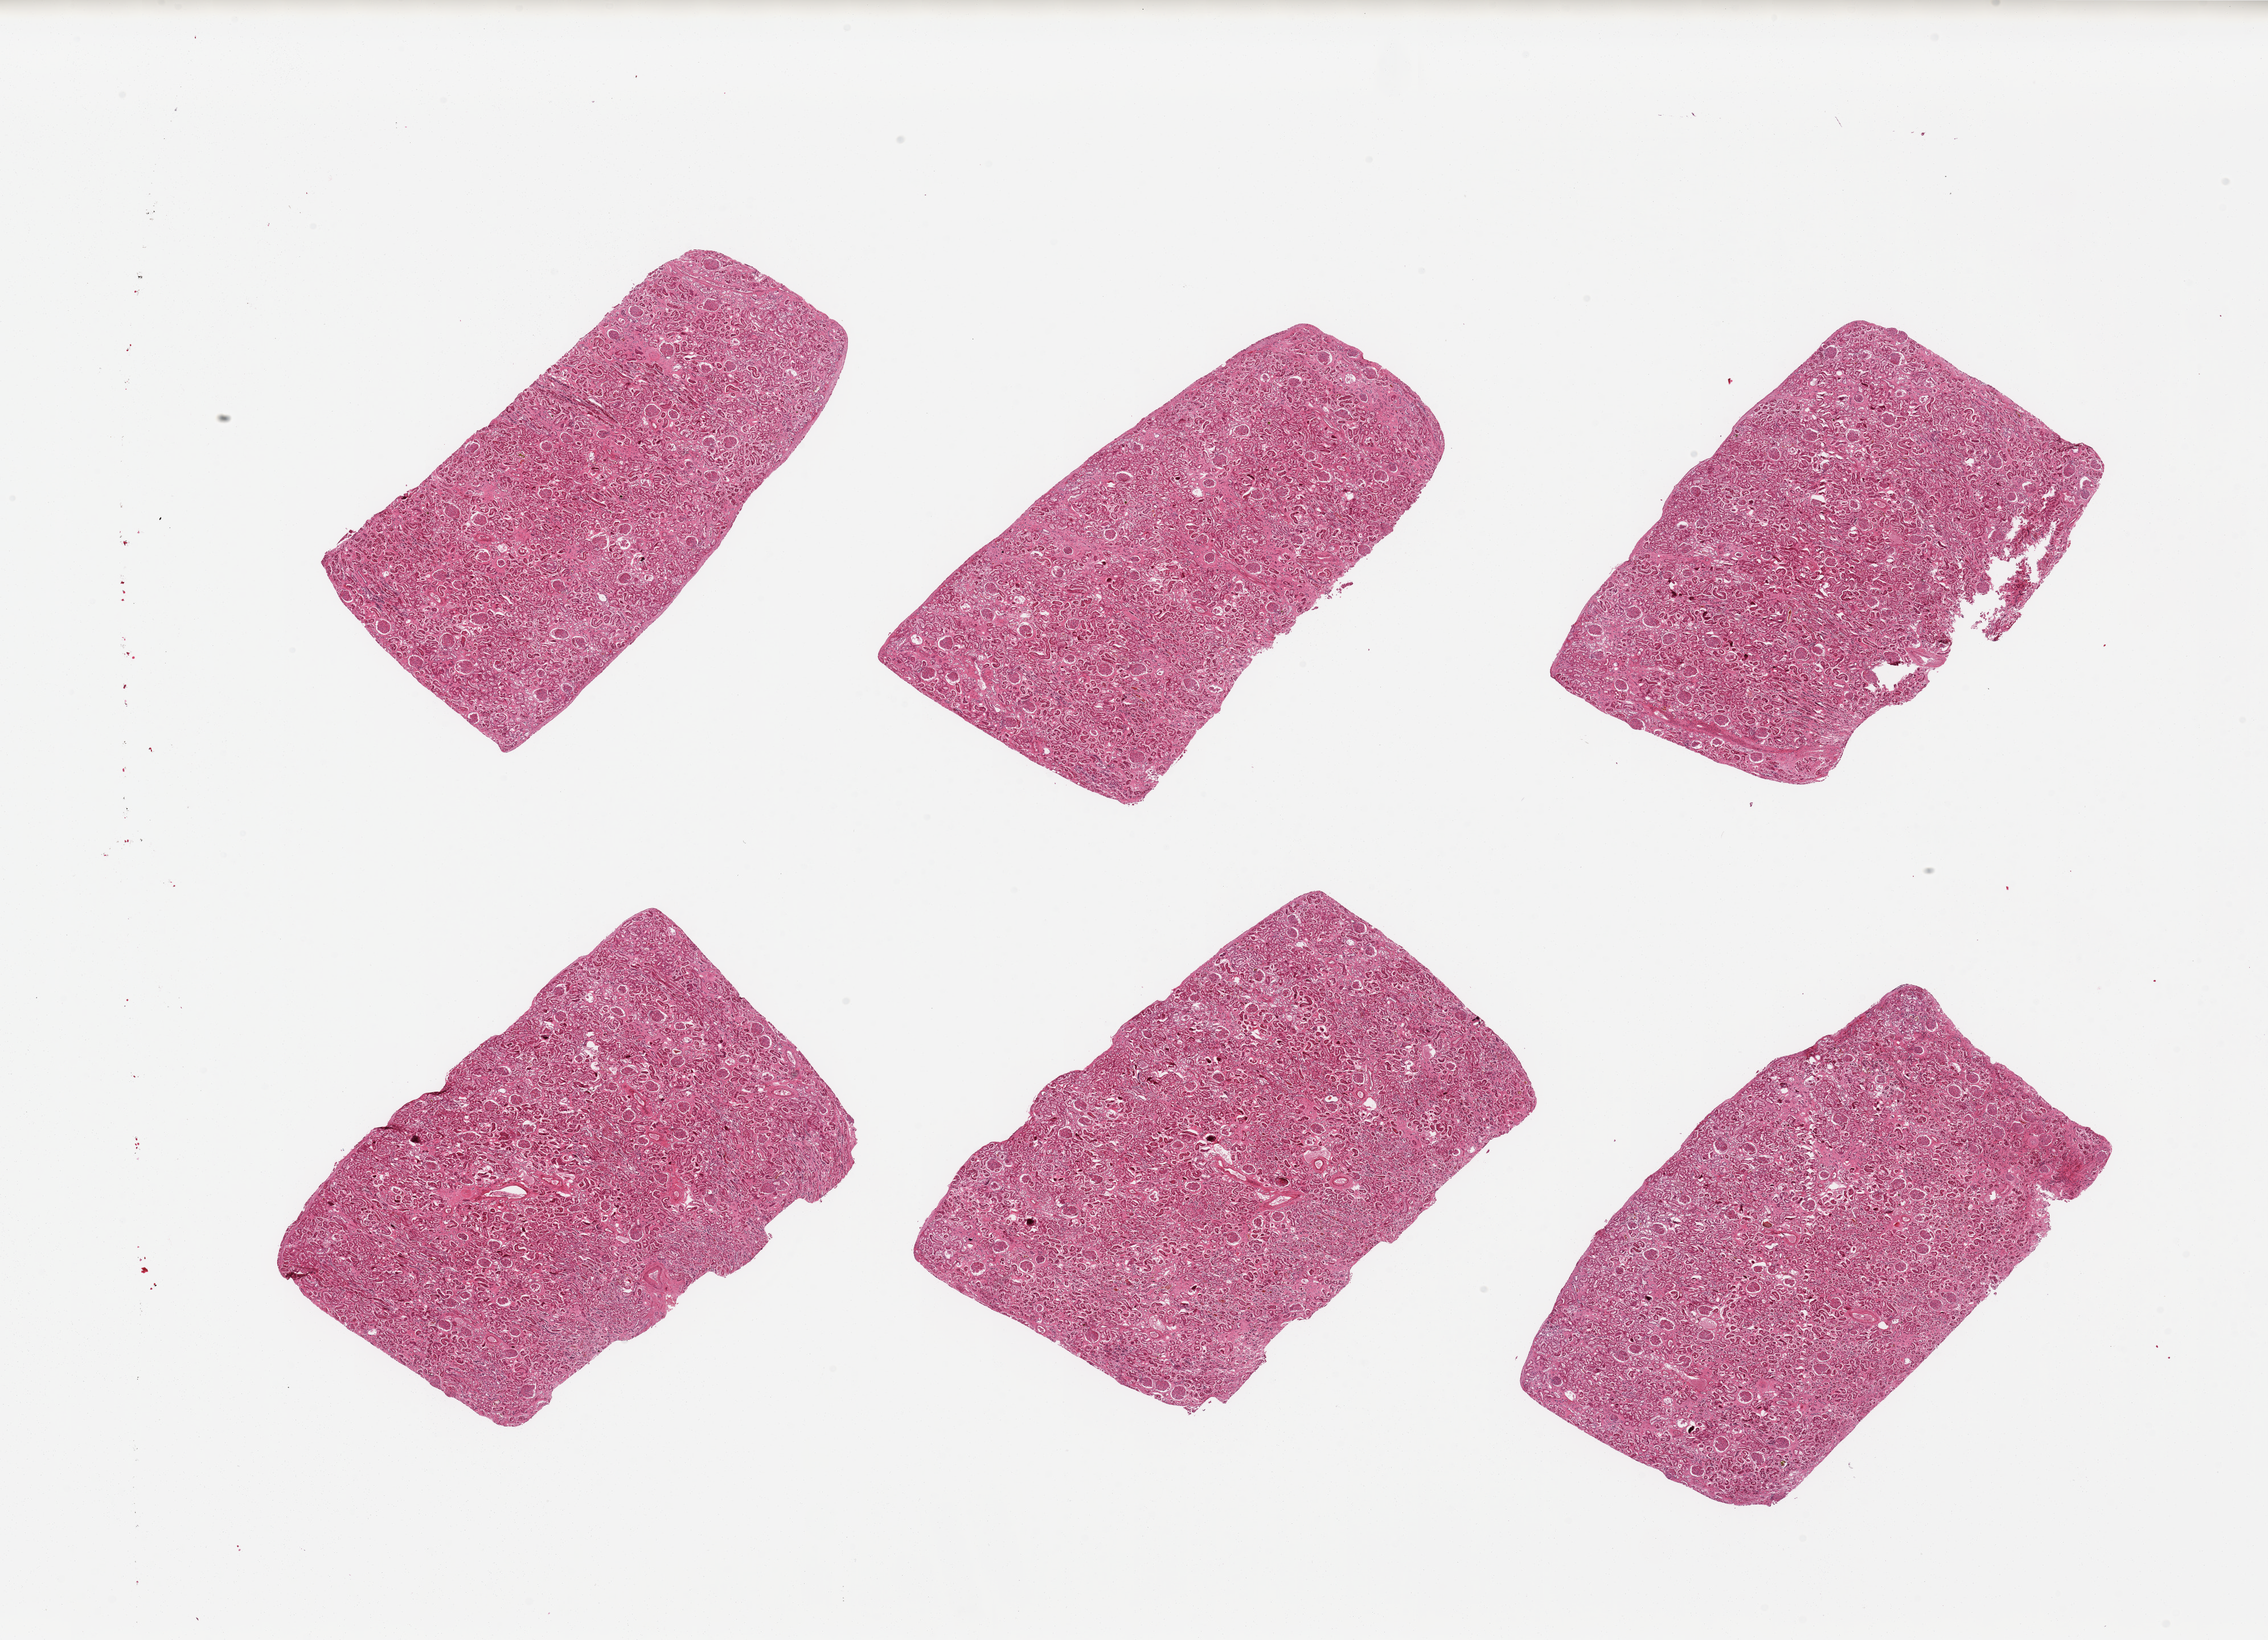
Whole-slide image, haematoxylin and eosin stain — shown as a low-resolution overview of the whole scanned area (about 31.5 x 22.8 mm, from a 20x scan); PAXgene-fixed paraffin-embedded (PFPE) section; sampled site (target tissue): renal cortex; tissue donor sample. Donor sex: male.
• reviewer comment on this tissue sample: 6 pieces, glomeruli present; moderately advanced tubular autolysis